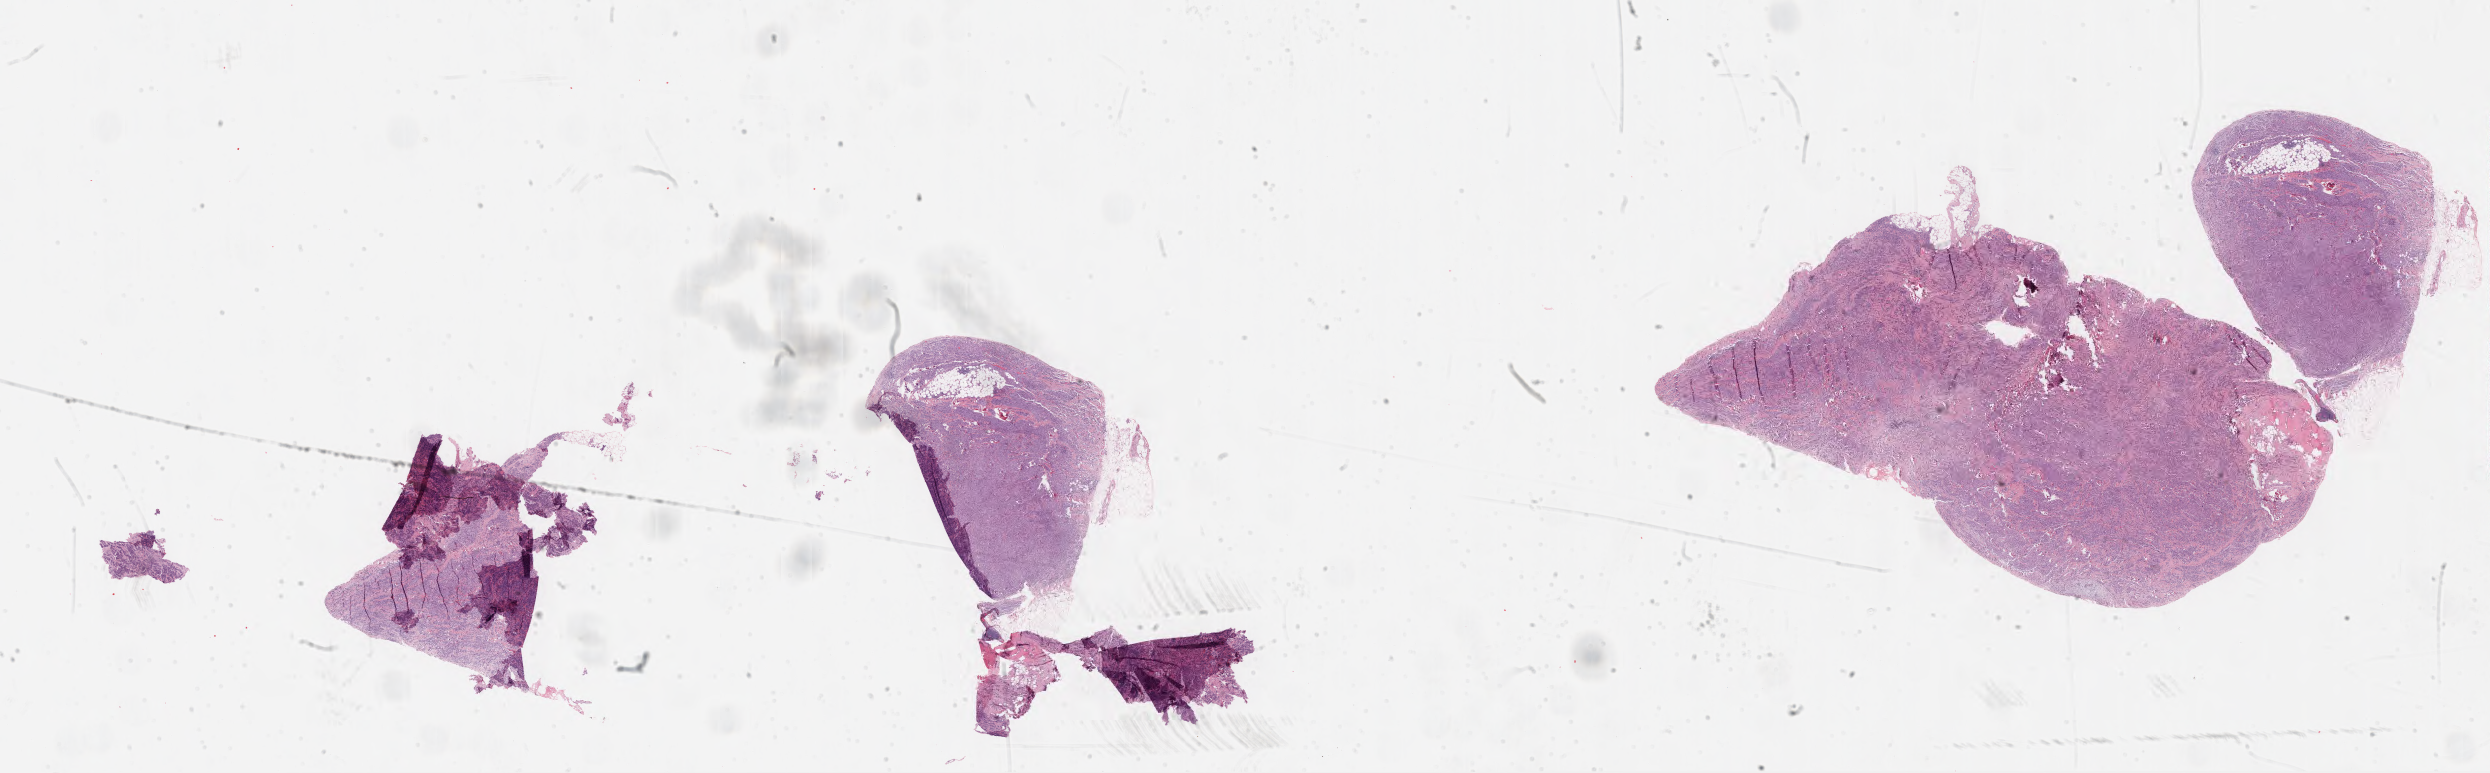
H&E whole-slide image, a low-resolution overview of the entire scanned area, about 40.2 x 12.5 mm, FFPE section, primary tumour sample from the mesothelium. Male patient; age at initial diagnosis 71 years.
Diagnosis: Epithelioid mesothelioma, malignant. Laterality: right. AJCC pathologic stage: III (6th edition).